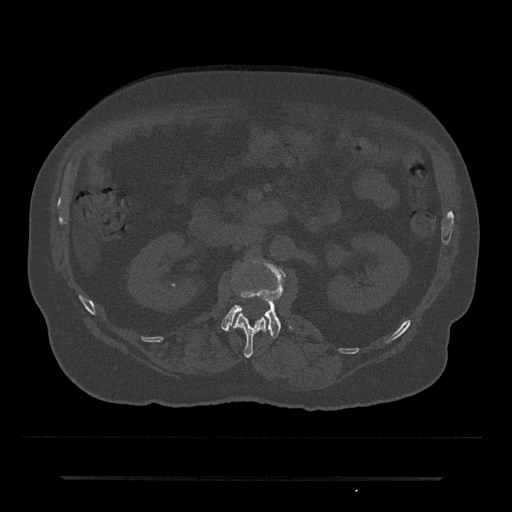
CT including the spine, one axial slice; position 37 of 797 along the scan axis; bone window (W 1800 / L 400 HU); 512 × 512 image matrix, field of view 437 × 437 mm. Male patient, age 69 years. Case-level facts recorded for this patient, not image findings: primary cancer: prostate.
Annotated regions visible in this slice (semi-automatic segmentation, software-assisted and operator-edited):
- L1 vertebra: box from (x=233, y=313) to (x=267, y=358) px
- L2 vertebra: (x=221, y=261)–(x=292, y=339)